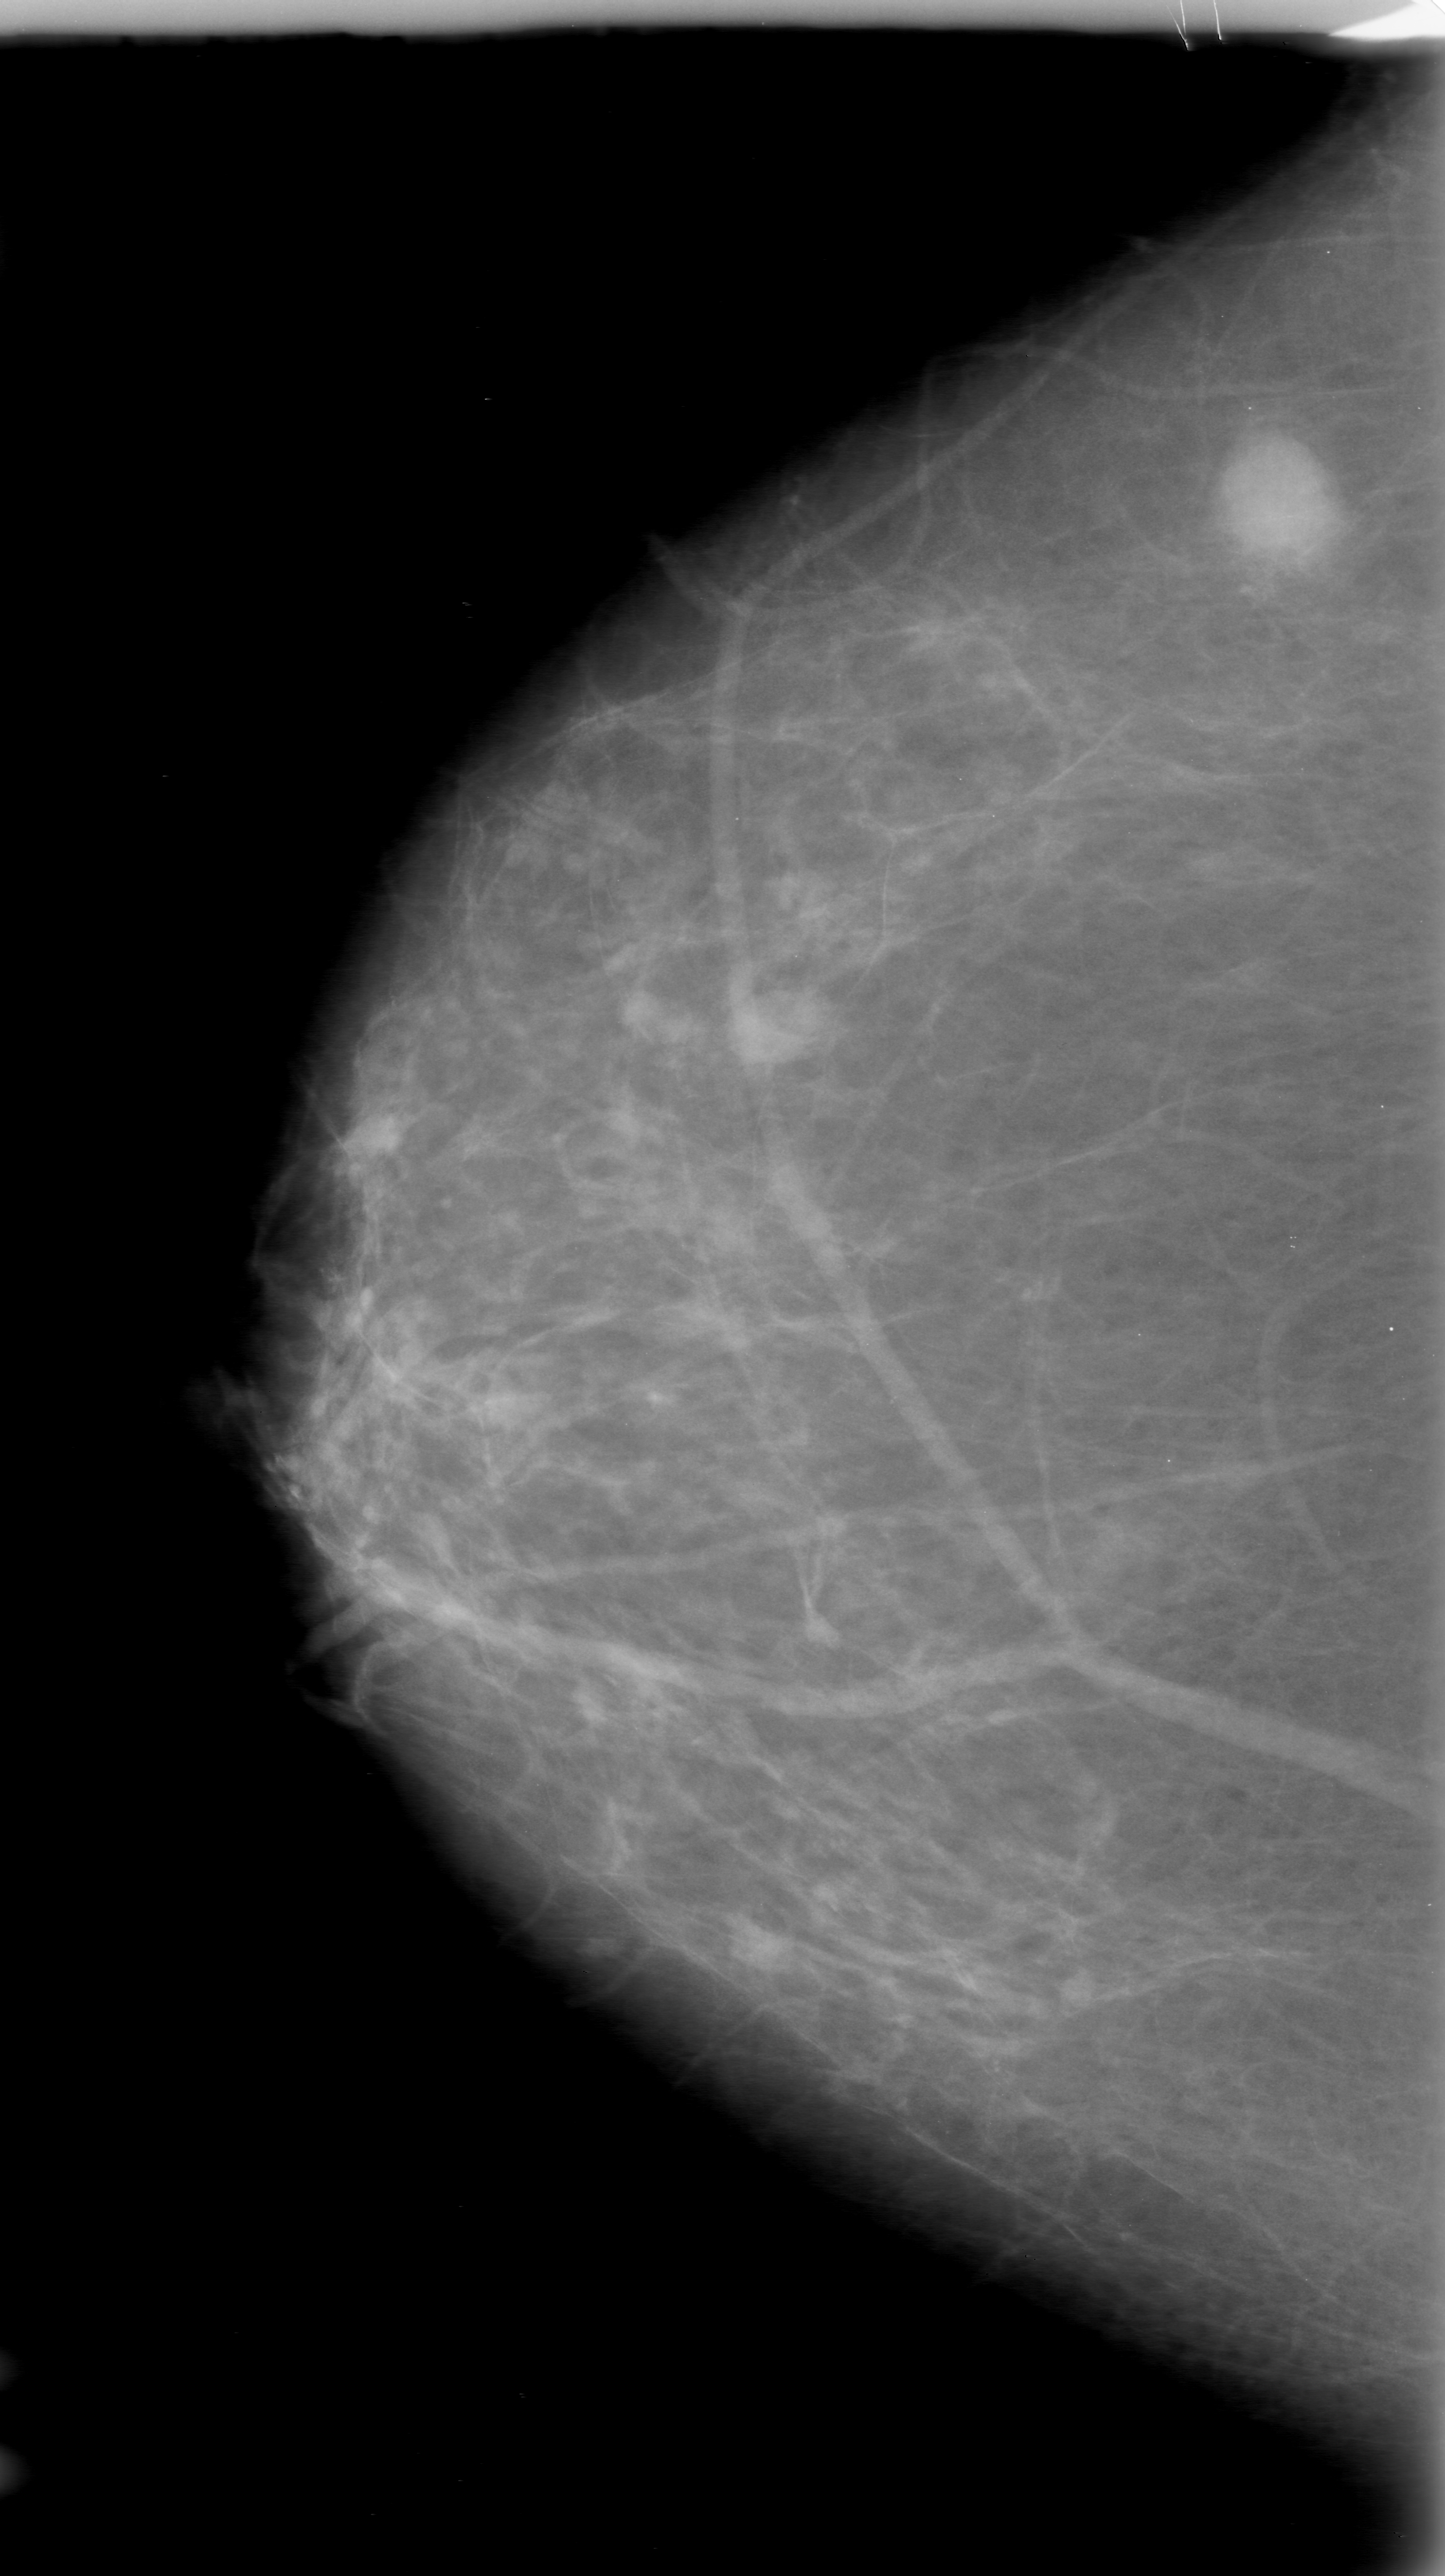
Digitized screen-film mammogram. Right breast. Craniocaudal (CC) view. Breast composition: scattered fibroglandular densities (BI-RADS density category 2 of 4). 1445 × 2576 image matrix.
Marked abnormalities (boxes around the expert regions of interest):
- mass, shape round, margins ill defined; BI-RADS assessment category 5; subtlety rating 5 on a 1 (subtle) to 5 (obvious) scale; pathology result (as recorded, not read from the image): malignant: bounding box [x1, y1, x2, y2] px = [1196, 416, 1362, 606]